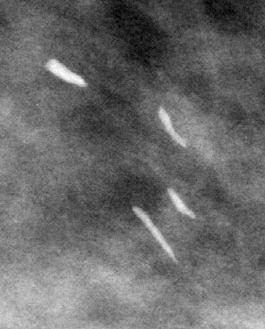
Cropped region of a digitized screen-film mammogram centred on a radiologist-marked abnormality; left breast; CC view; BI-RADS breast density category 3 (scale 1–4).
Marked abnormality: calcifications, morphology large rodlike / round and regular, distribution regional; BI-RADS assessment category 2; benign without callback (not worked up further).